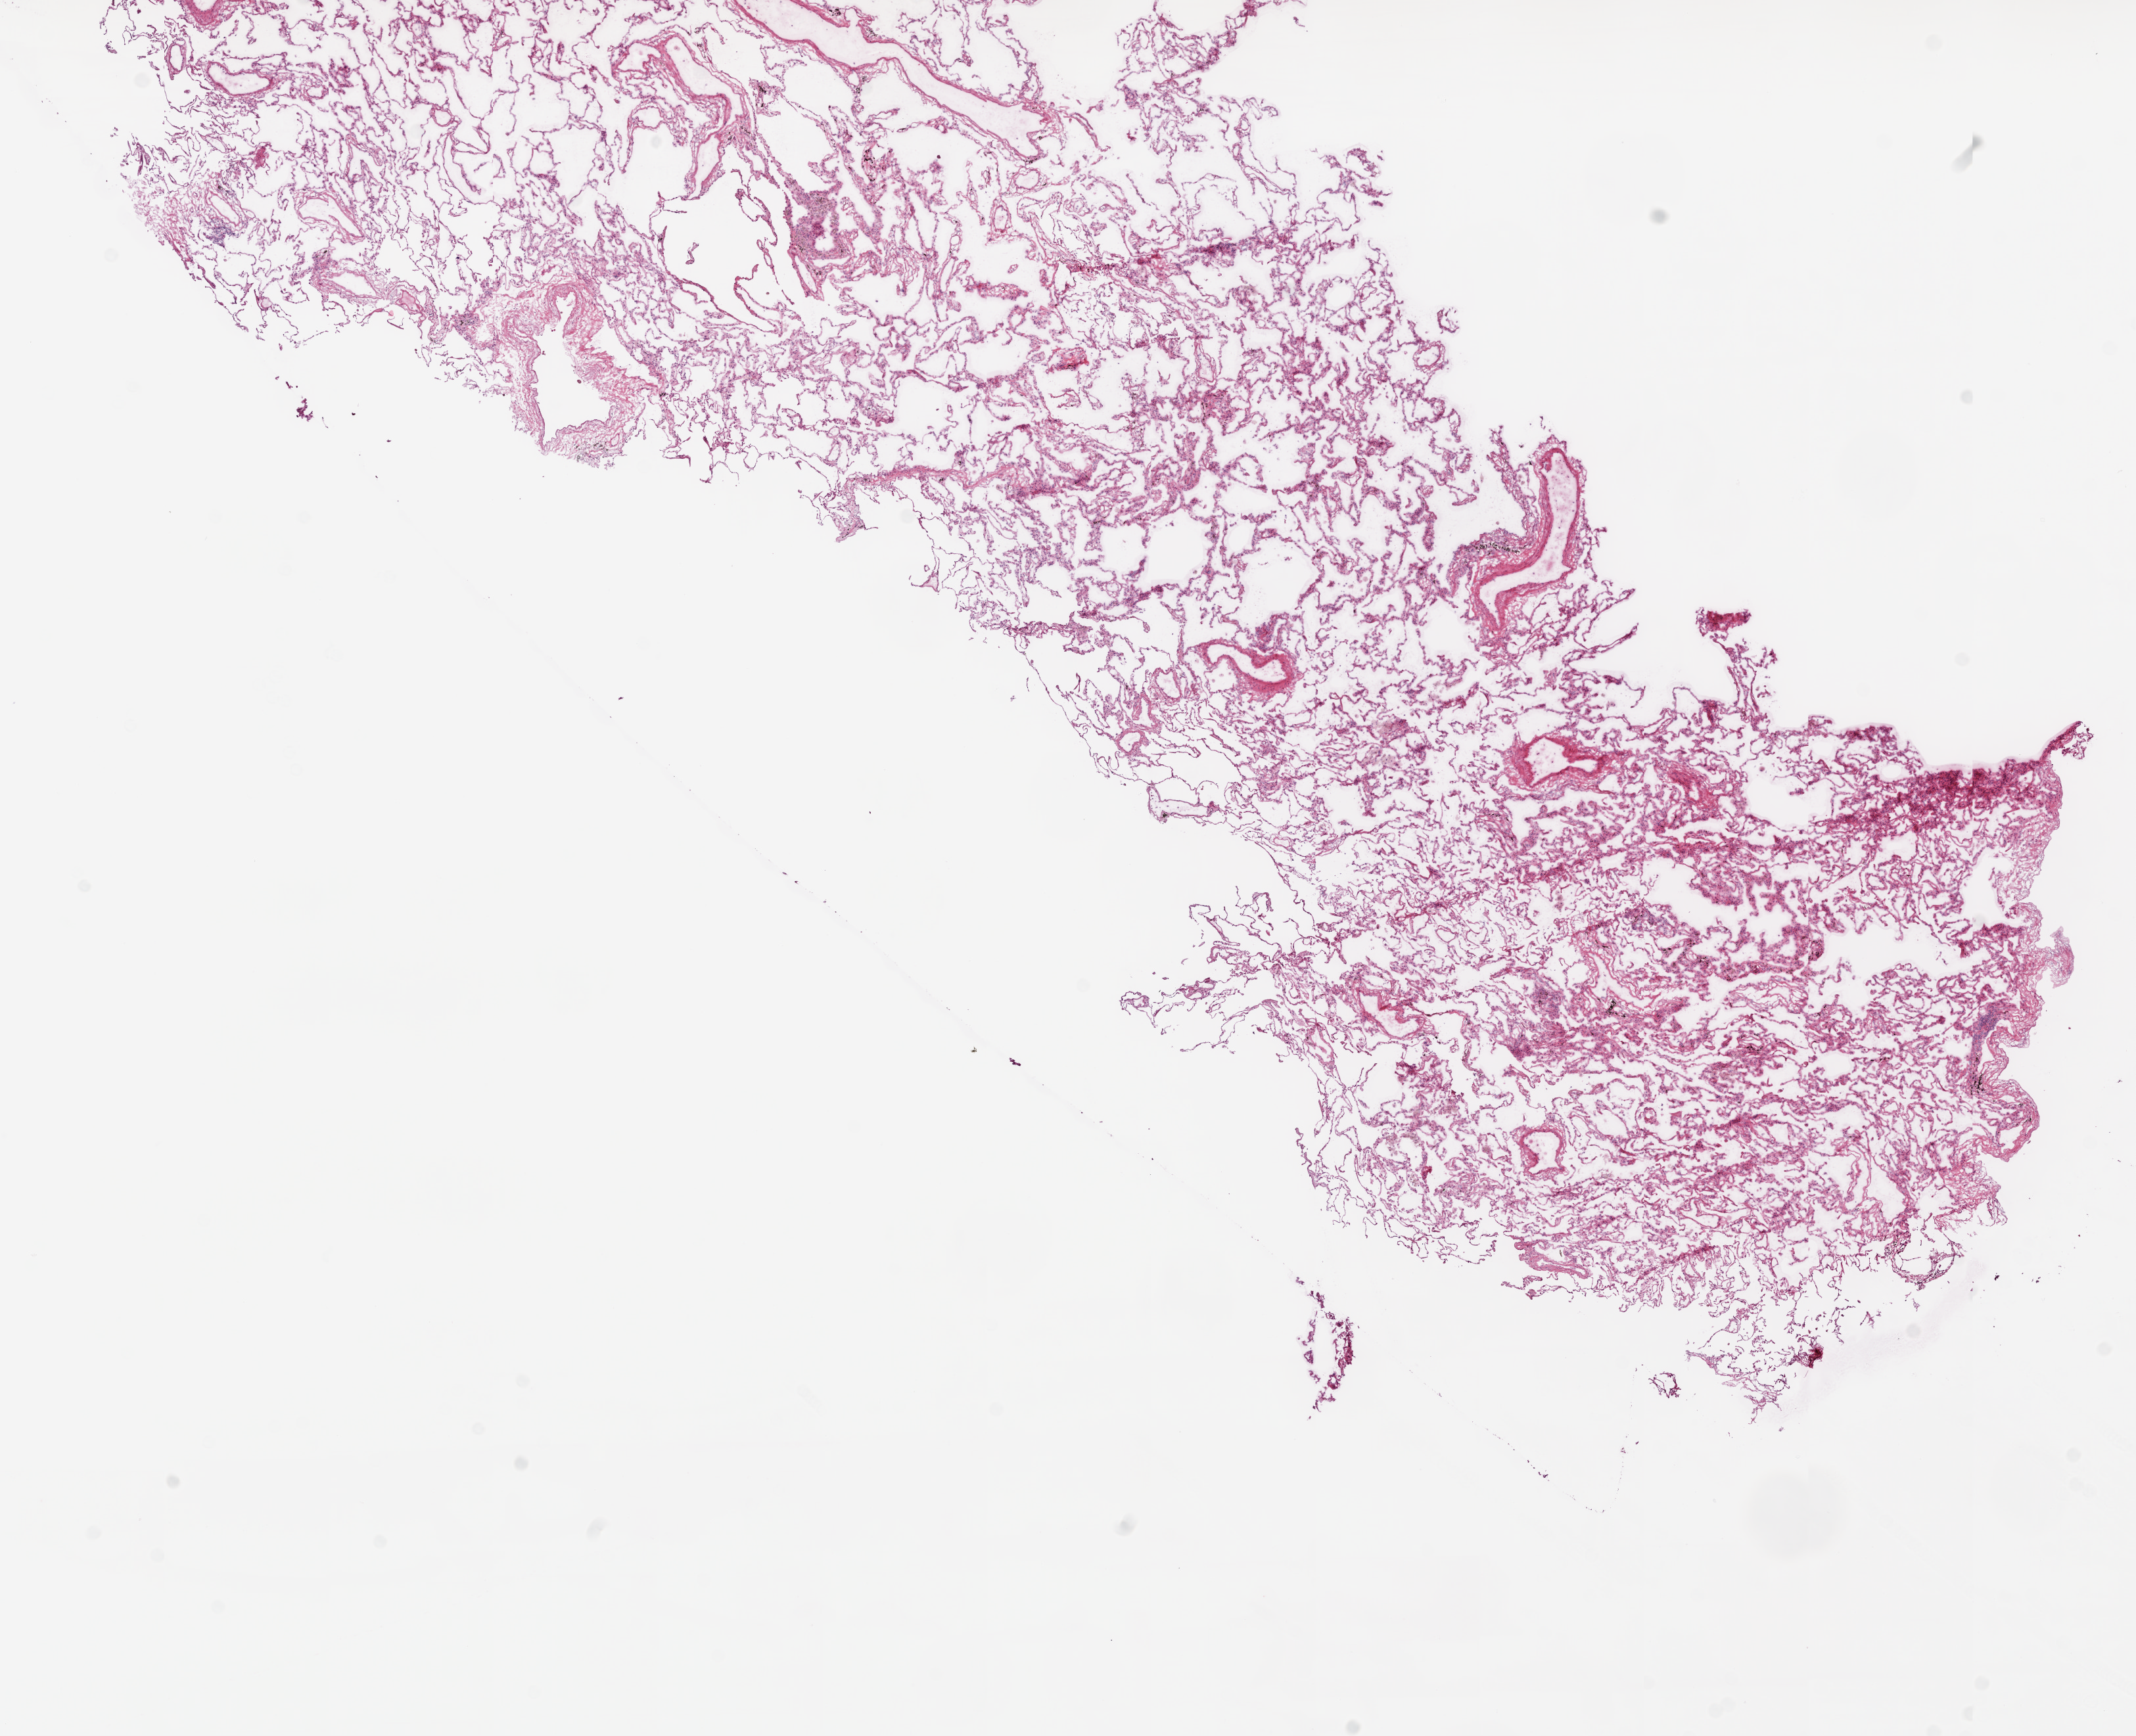
Whole-slide histology image, Hematoxylin and eosin (H&E) stained — shown as a low-resolution overview of the whole scanned area (about 13.0 x 10.6 mm), frozen section from the top of the tissue portion, solid tissue normal (non-tumour tissue) sample from the lung. Male patient; age at initial diagnosis 81 years.
- this section: solid tissue normal sample (biorepository sample class)
- patient diagnosis: Squamous cell carcinoma, NOS (upper lobe, lung)